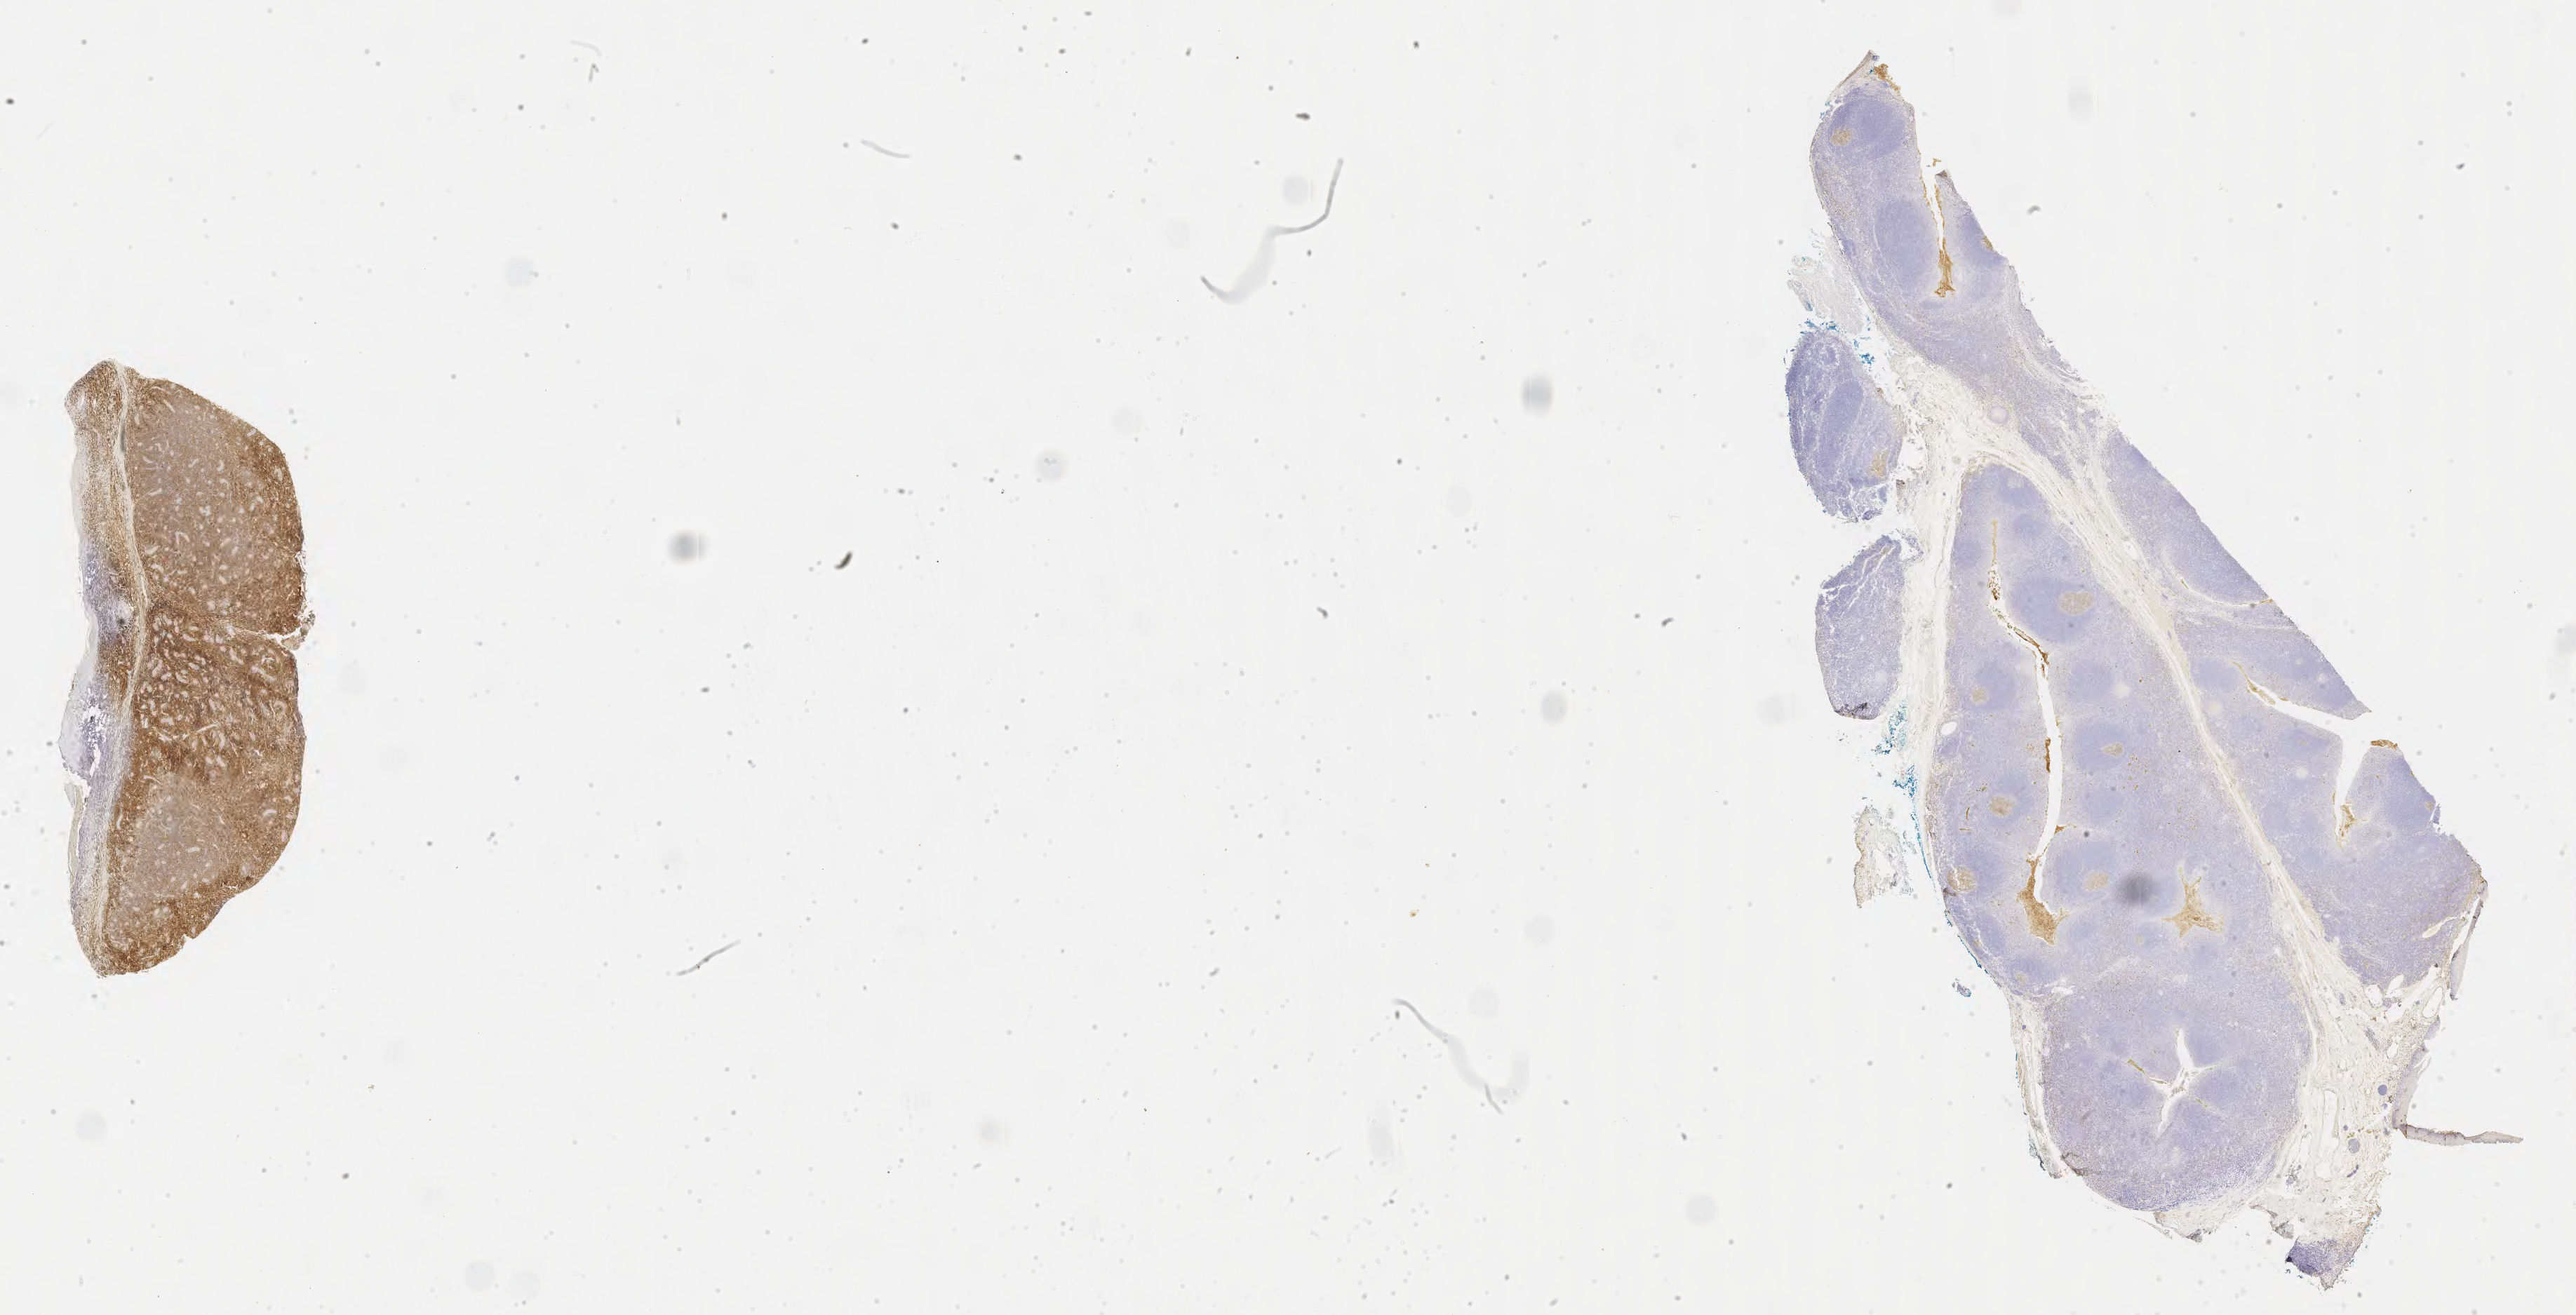
Whole-slide image, immunohistochemical stain for CD10, a low-resolution overview of the entire scanned area, about 29.7 x 15.2 mm, tumor tissue, site: testis. Male patient; age at initial diagnosis 8 years.
Diagnosis: Burkitt lymphoma, NOS.